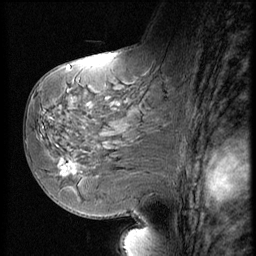
Breast MRI (dynamic contrast-enhanced), one sagittal slice; dynamic contrast-enhanced series, image 2 of 3 at this slice position (ordered by acquisition); 1.5 T; TE 4.2 ms, TR 9 ms; 2.5 mm slice thickness; 256 × 256 image matrix, field of view 180 × 180 mm. Patient: female, 58 years. From the clinical record (not read from this slice): setting: breast cancer imaged before/during neoadjuvant chemotherapy; receptor status: HR-positive, HER2-negative.
Annotated regions visible in this slice (semi-automatic segmentation, software-assisted and operator-edited):
- analysis volume of interest (the breast-tissue region the enhancement analysis was run in; not a lesion): bounding box (x1, y1, x2, y2) in pixels: (51, 147, 96, 185)
- tumour enhancement mask (voxels above the 140 % enhancement threshold inside the analysis volume of interest): (59, 158, 78, 176)